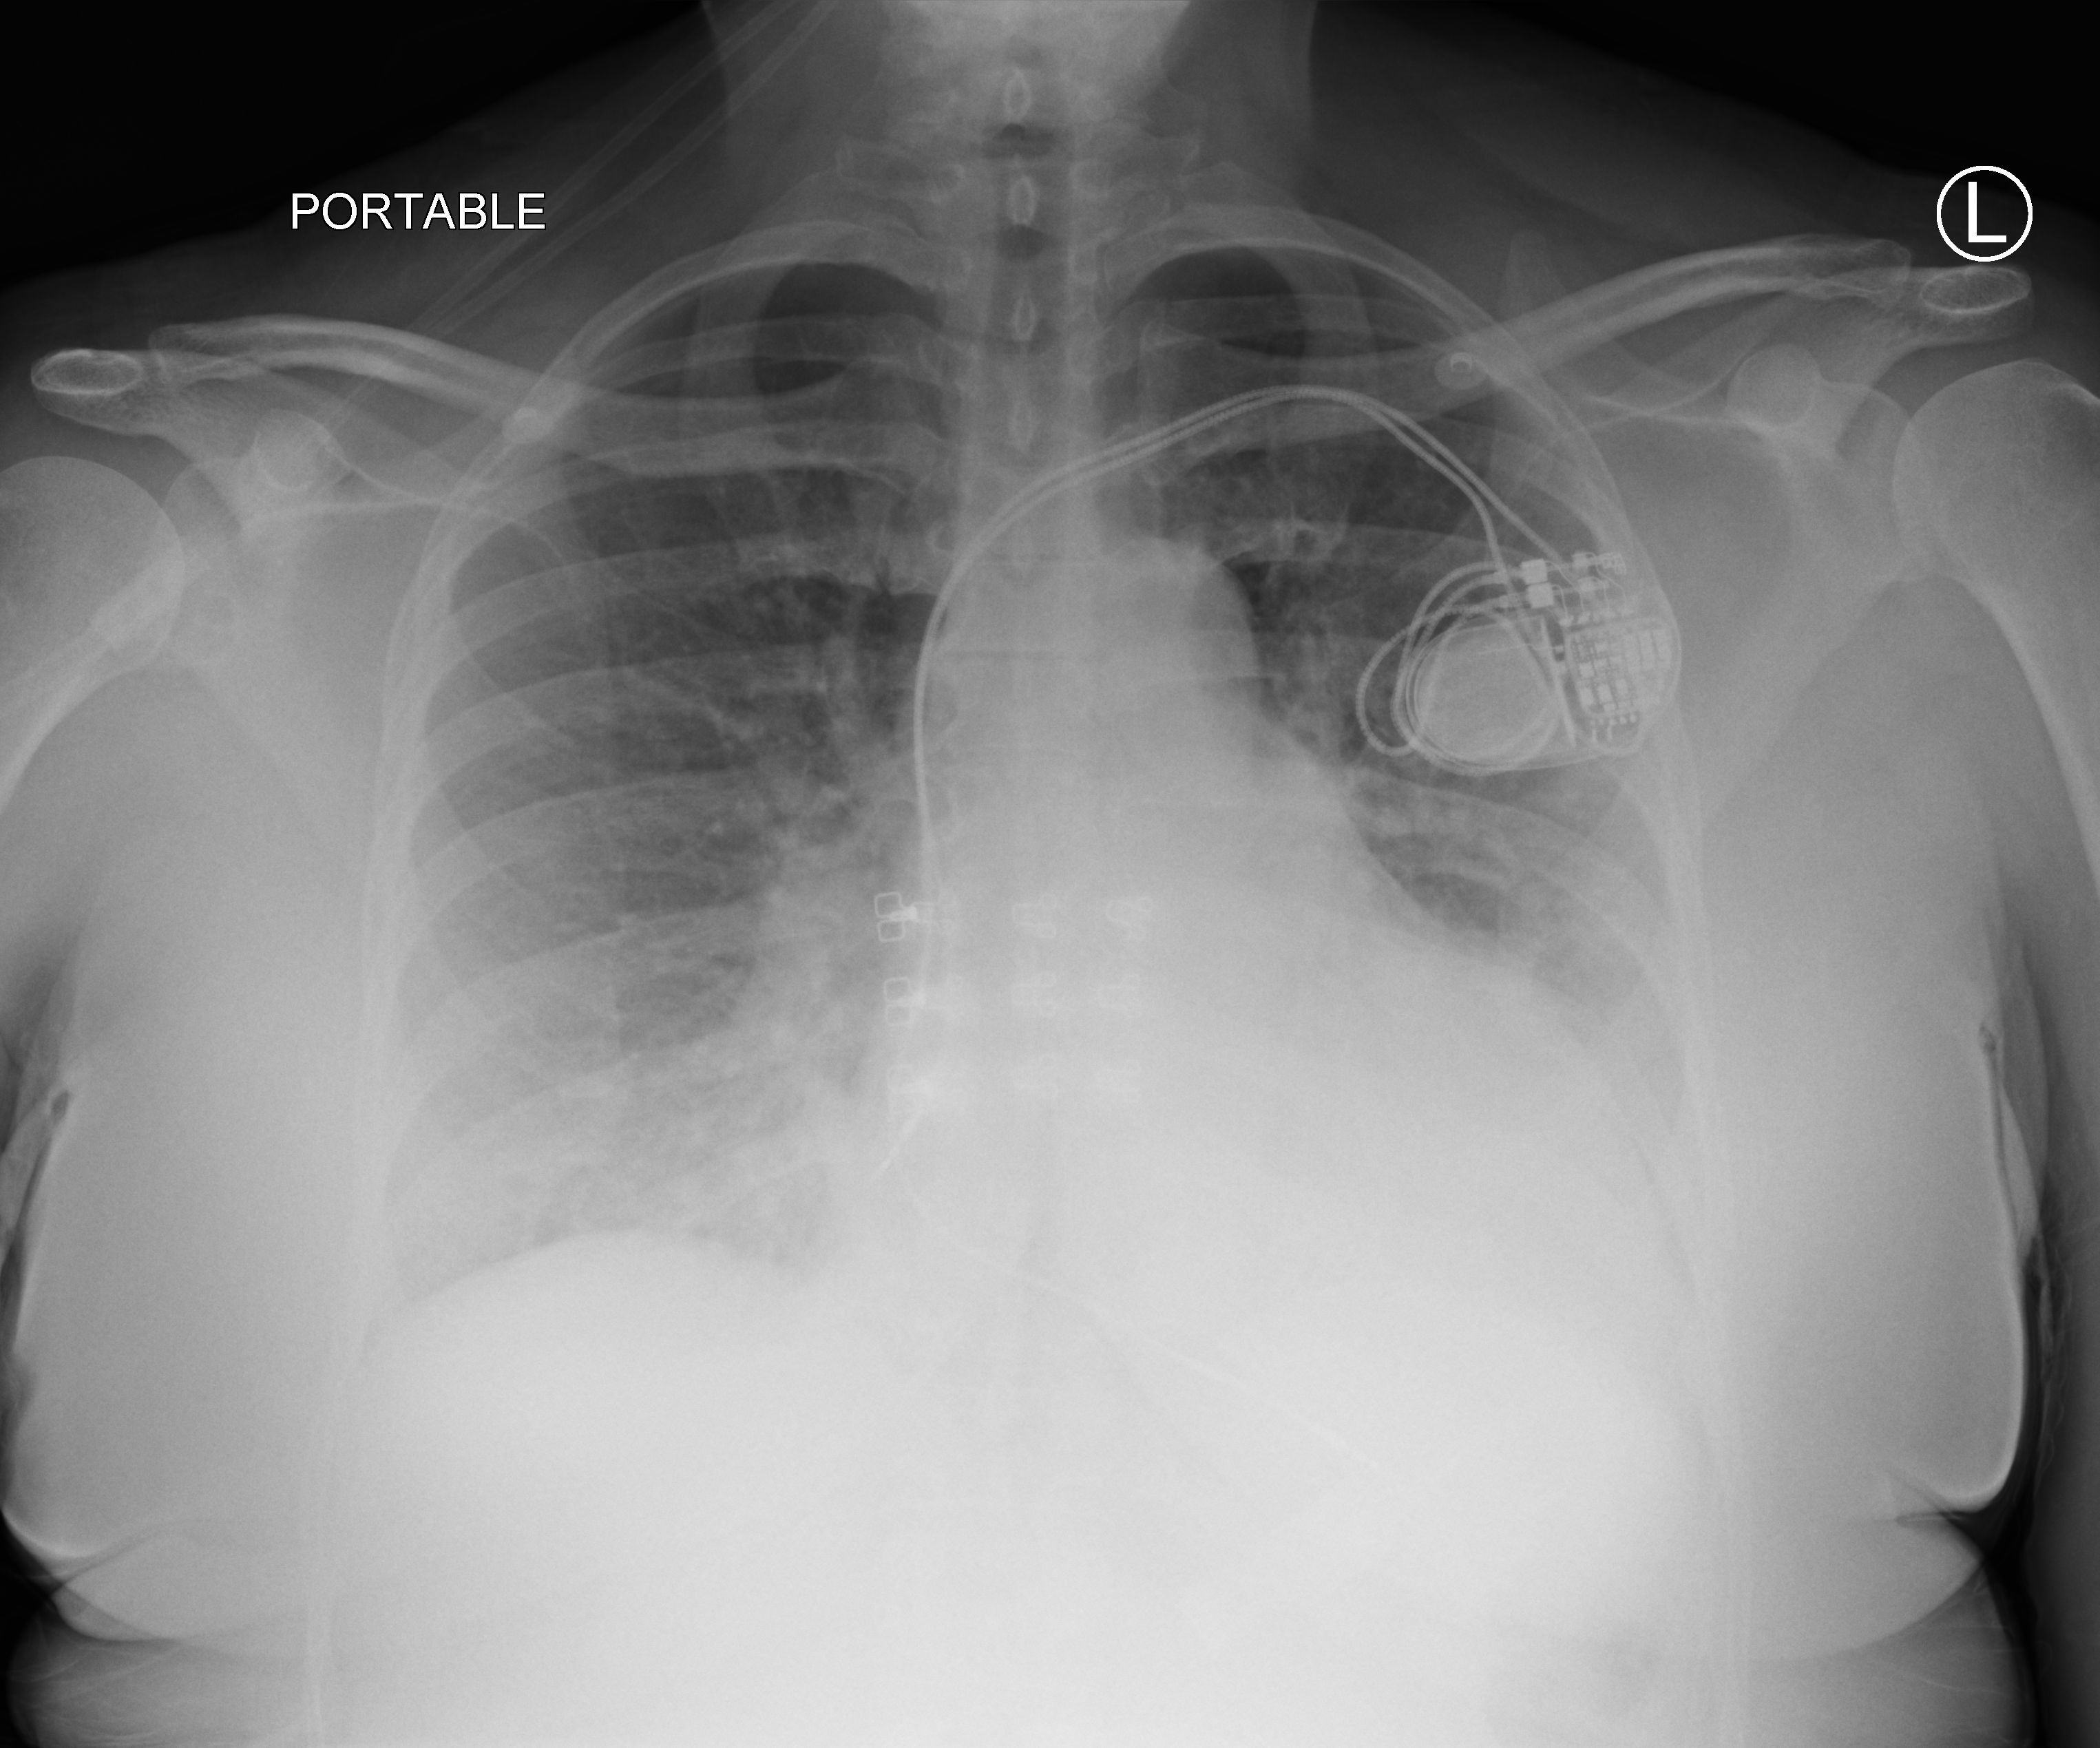
Bedside chest radiograph (computed radiography). Patient hospitalised with COVID-19; female, aged 18–59 years.
From the hospital-stay record, not from the radiograph (when in the stay this image was taken is not recorded): mechanically ventilated during this hospital stay: no.